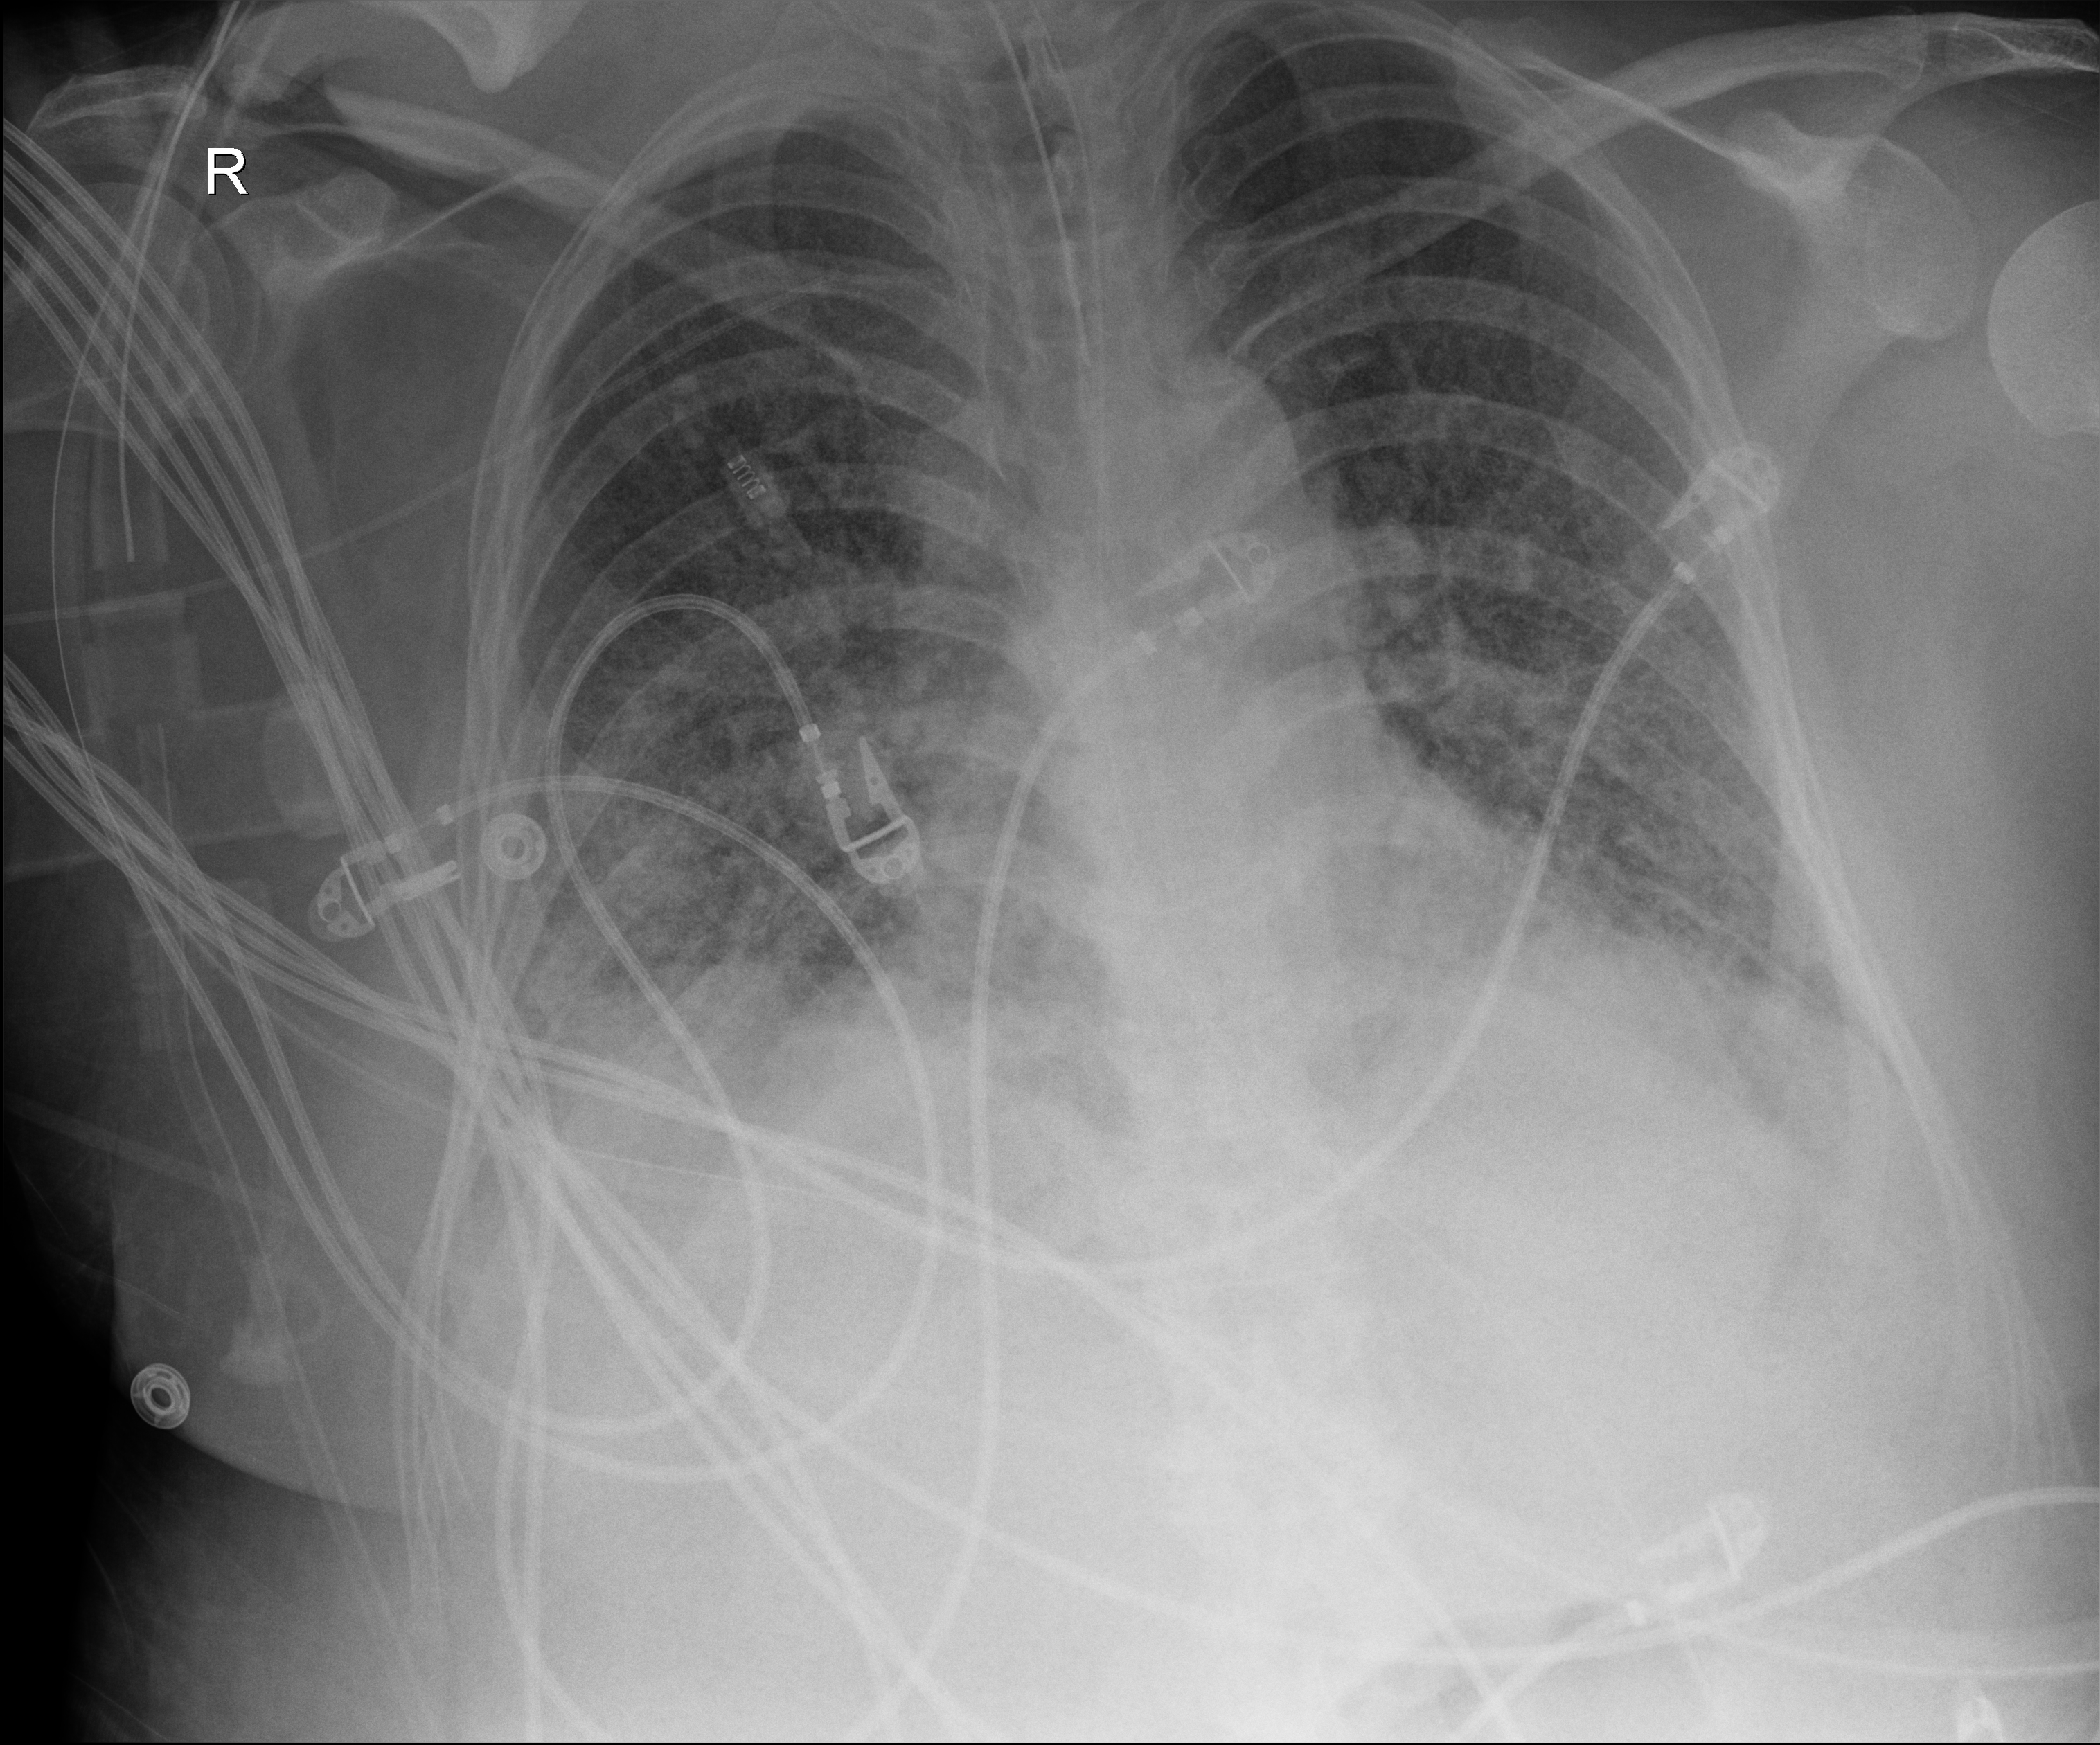
Bedside chest radiograph (digital radiography); anteroposterior (AP) projection. Patient hospitalised with COVID-19, aged 18–59 years.
Admission-level facts for this patient (not findings on this image; timing relative to this image not recorded): admitted to intensive care during this hospital stay: yes.